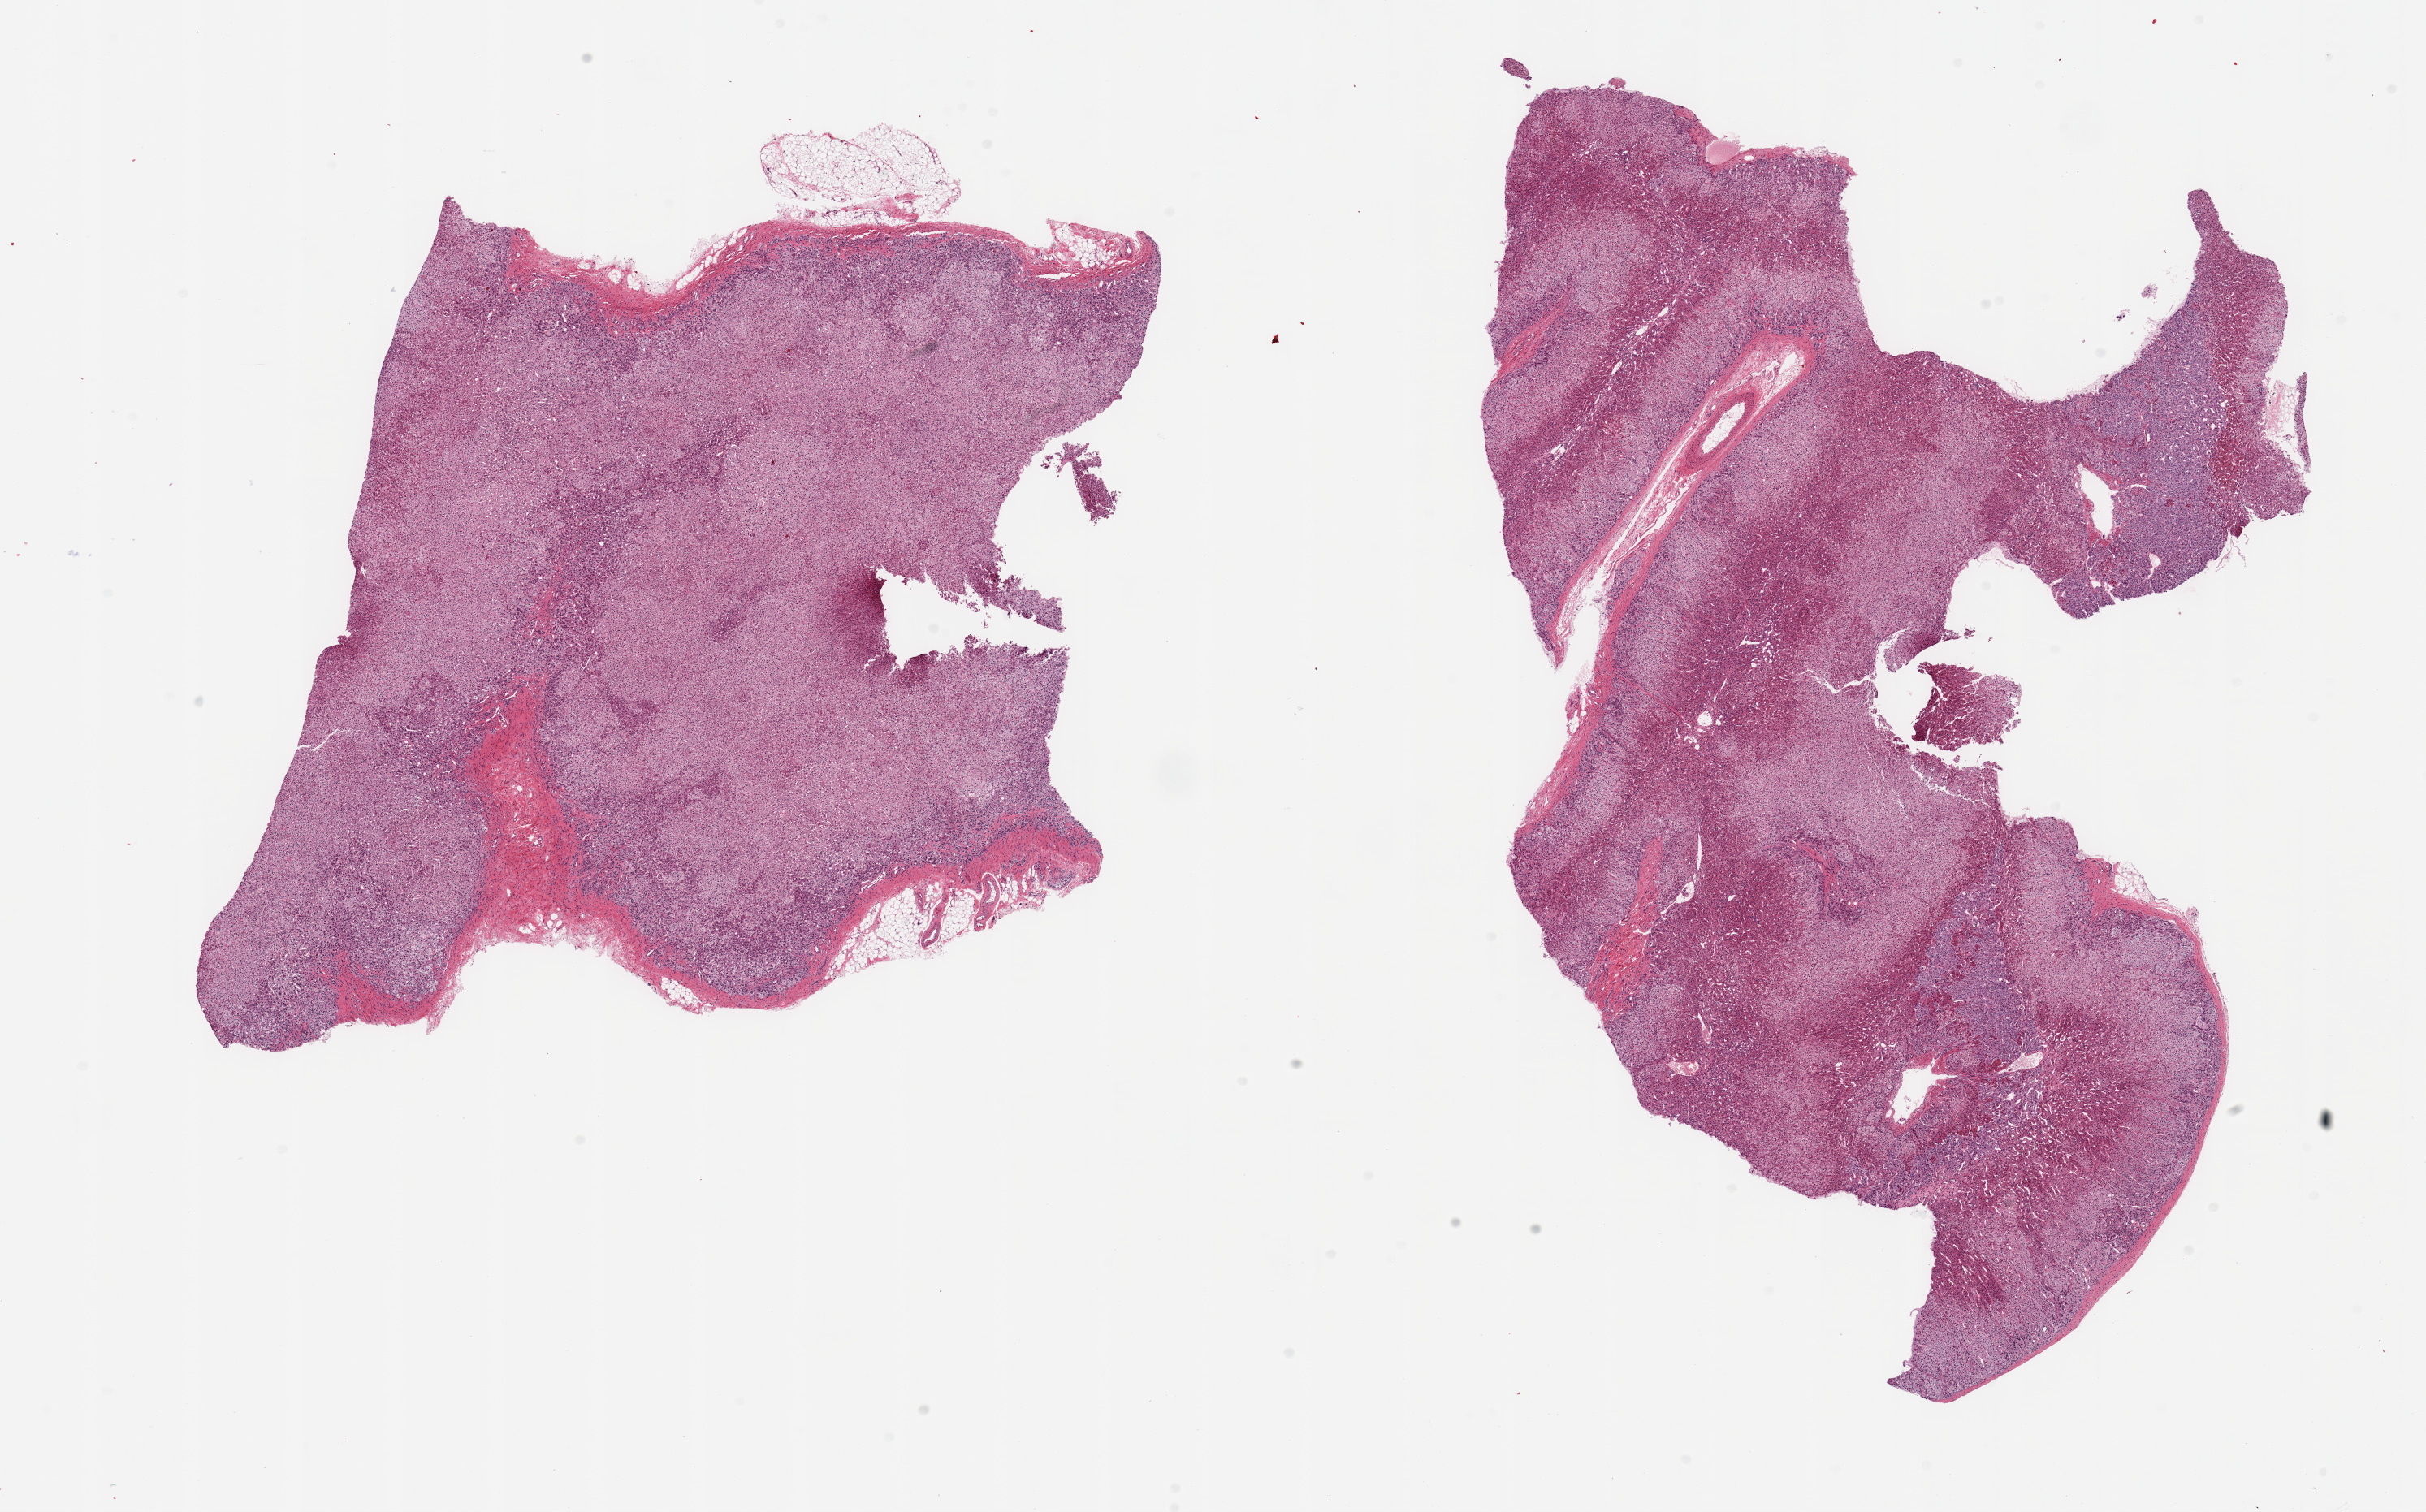
Whole-slide image, hematoxylin and eosin (H&E) stain, whole scanned area (about 23.6 x 14.7 mm) shown as a low-resolution overview. PAXgene-fixed, paraffin-embedded tissue. Sampled site (target tissue): adrenal gland. Donor tissue sample. Donor: female.
* pathologist's review note for this sample: 2 pieces; cortex and medulla, trivial amount of attached fat